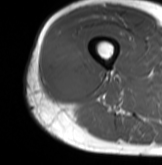
MRI of an extremity soft-tissue mass, one axial slice; MR volume resampled by the dataset authors to the PET/CT grid (not the native acquisition matrix); 3.27 mm slice thickness; 162 × 165 image matrix, field of view 158 × 161 mm. Male patient. From the clinical record (not read from this slice): histological type: poorly differentiated synovial sarcoma; grade: high; site of the primary tumour: right buttock.
Structures marked on this image (expert contour drawn on MRI and transferred to this co-registered scan by the dataset authors):
- gross tumour volume including surrounding oedema: bounding box <45,31,92,99> (left, top, right, bottom; pixels)
- gross tumour volume (mass): <46,40,92,98>